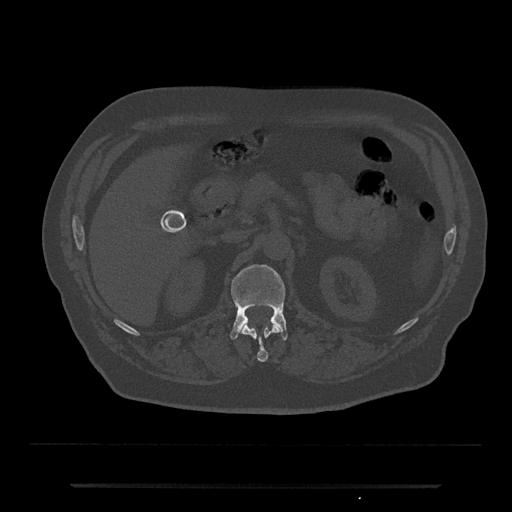
CT including the spine, one axial slice; slice 556 of 797 in the series (ordered by position); bone window (W 1800 / L 400 HU); 0.5 mm slice thickness; 512 × 512 image matrix, field of view 434 × 434 mm. Patient: male, 80 years. Case-level facts recorded for this patient, not image findings: primary cancer: prostate; vertebrae with lytic lesions (as recorded): L1, T11.
Structures marked on this image (semi-automatic segmentation, software-assisted and operator-edited):
- L1 vertebra: bounding box <230,265,288,340> (left, top, right, bottom; pixels)
- T12 vertebra: <242,324,280,362>